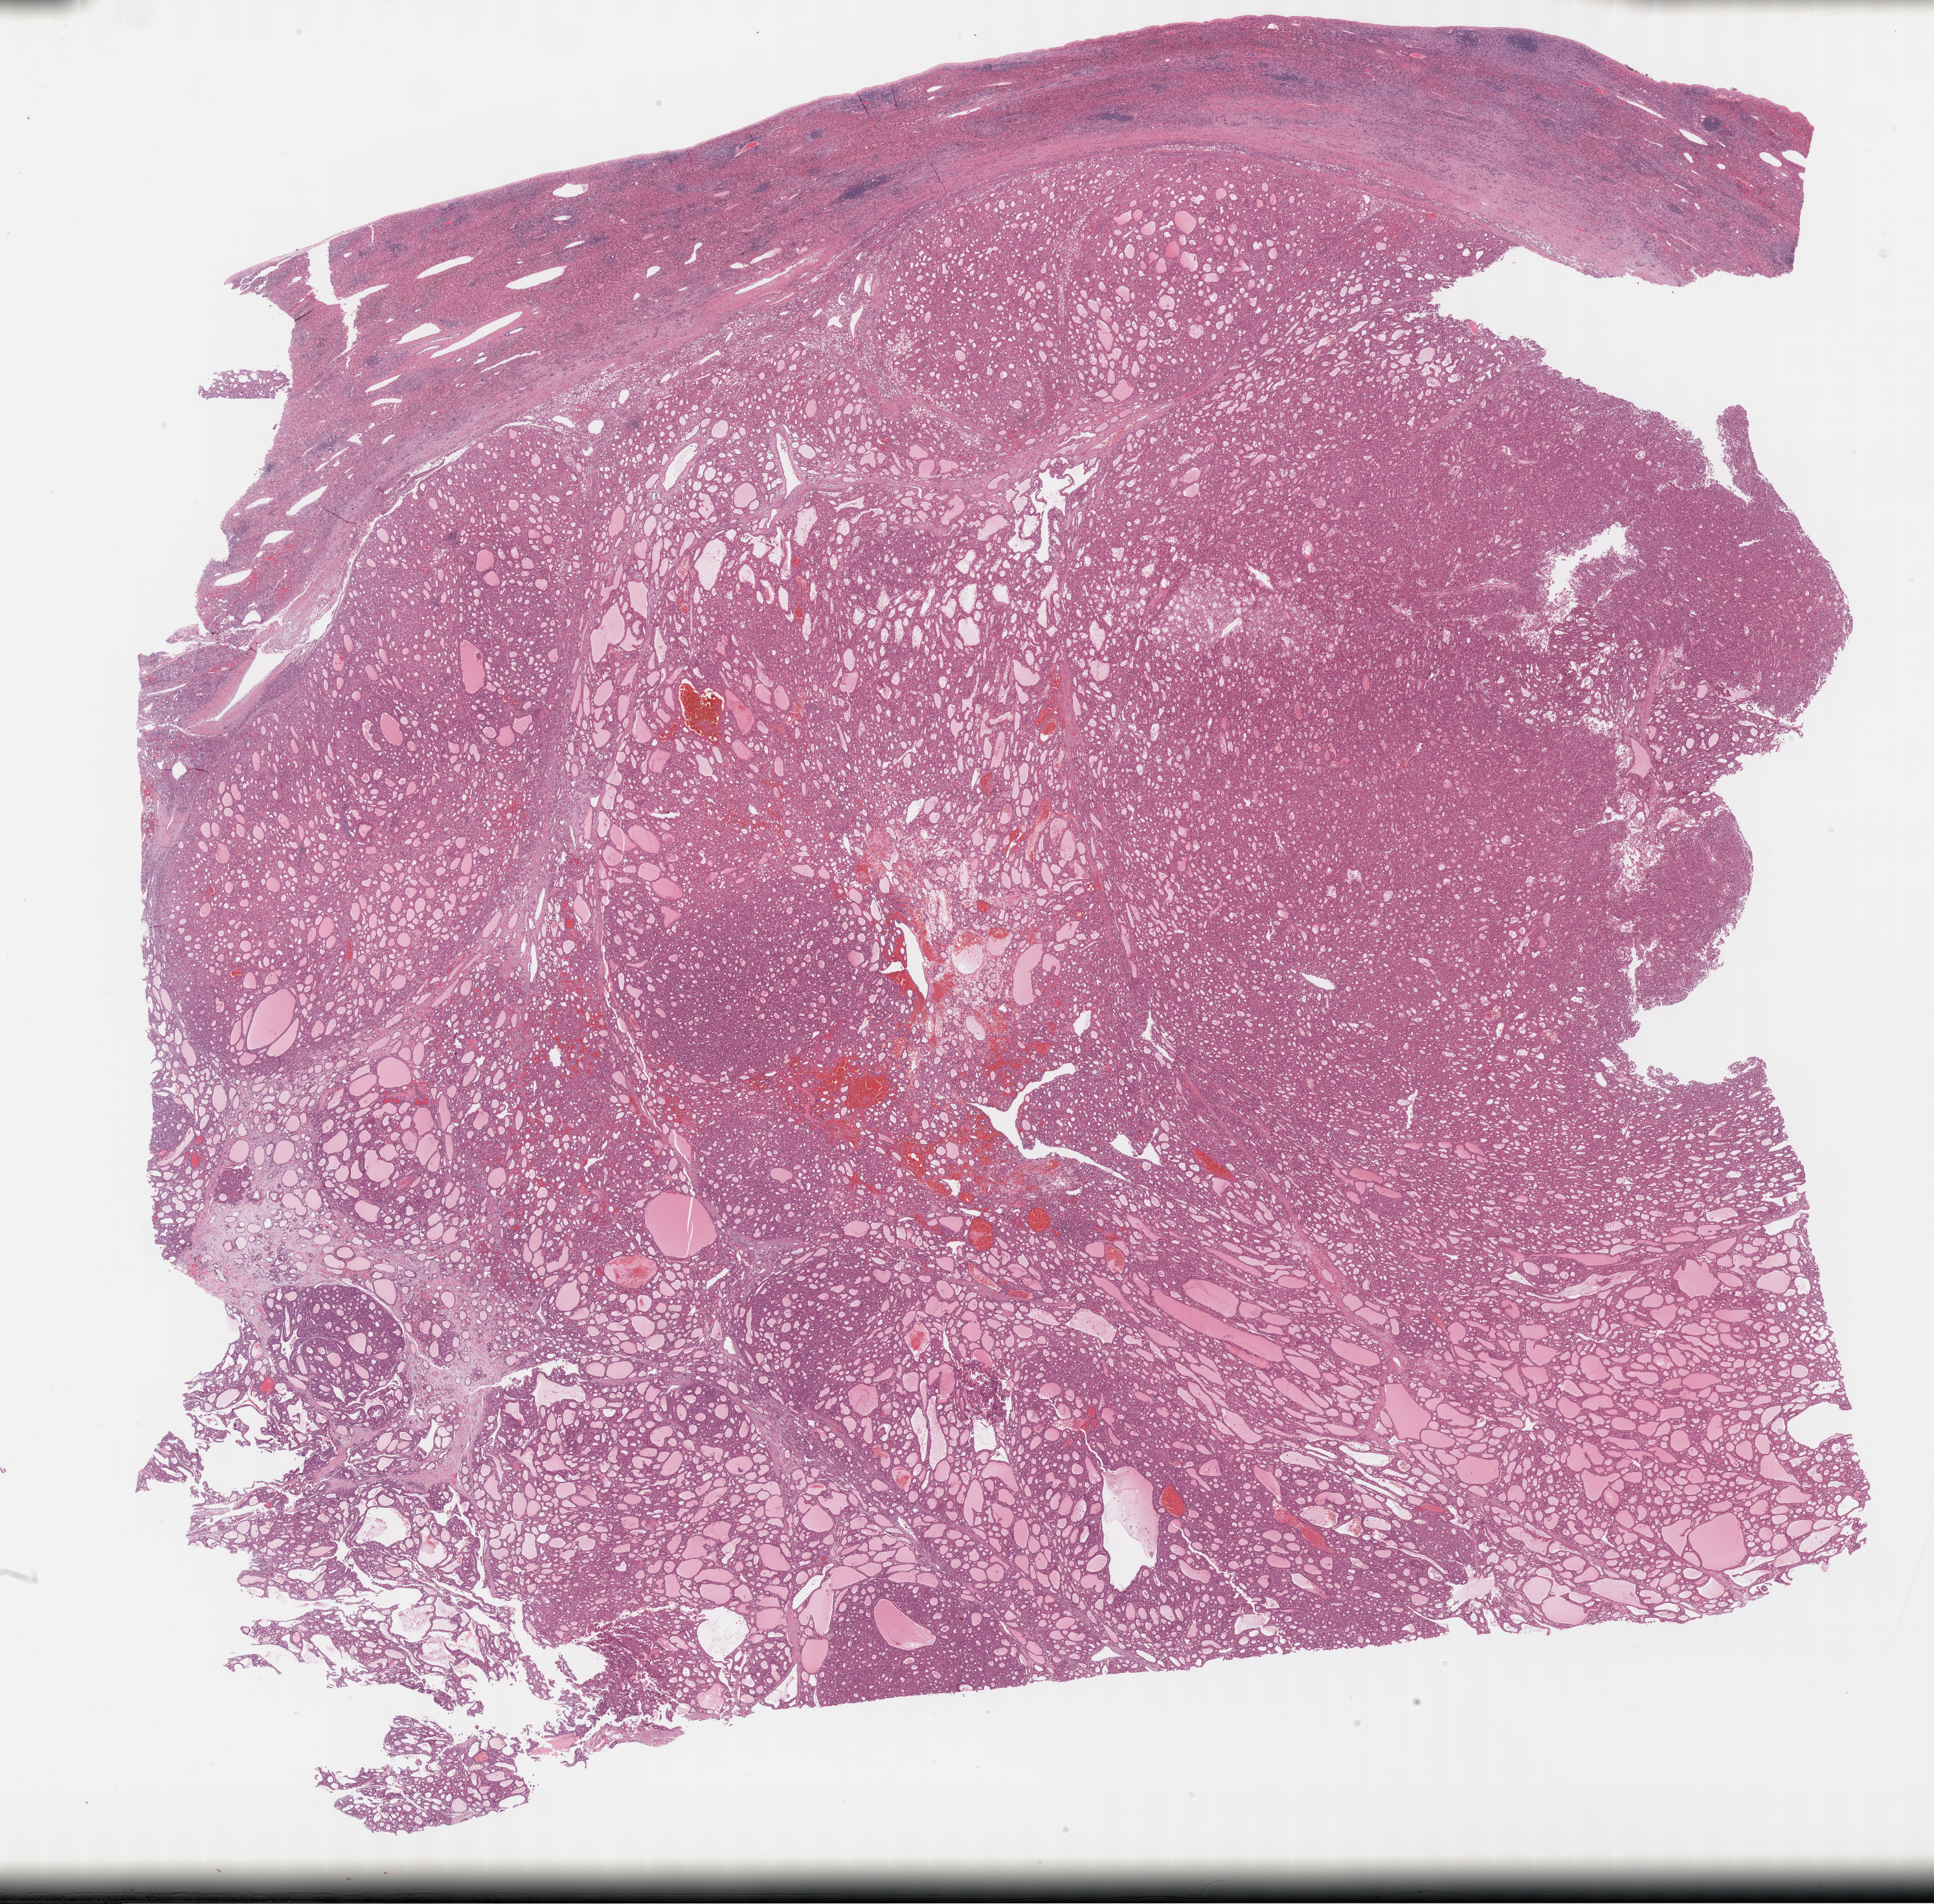
Whole-slide histology image, Hematoxylin and eosin (H&E) stained, a low-resolution overview of the entire scanned area, about 24.2 x 23.8 mm (from a 40x scan), FFPE section, primary tumour sample from the liver. Male, age 50 years at initial diagnosis. Histologic grade: G1 (well differentiated).
AJCC pathologic stage: I. Diagnosis: Hepatocellular carcinoma, NOS.